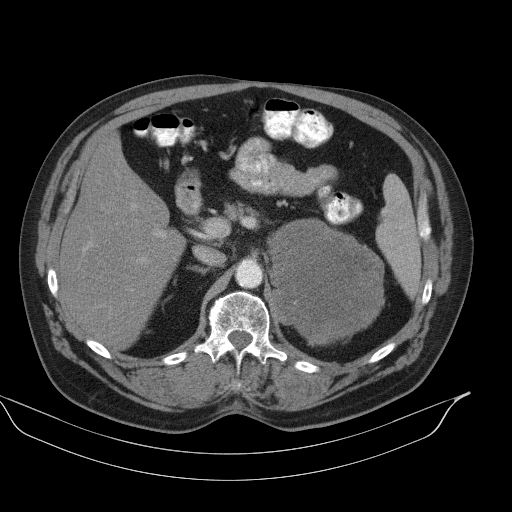
Contrast-enhanced abdominal CT, one axial slice. Slice 66 of 92 in the series (ordered by position). Reconstruction kernel B41s. 130 kVp. Soft-tissue window (W 400 / L 40 HU). 512 × 512 image matrix, field of view 449 × 449 mm. Male patient, age 56 years. Case-level facts recorded for this patient, not image findings: diagnosis: adrenocortical carcinoma; tumour side: left adrenal; tumour size at pathology: 15 cm; Ki-67 index: 35 %; stage (as recorded): 4.
Annotated regions visible in this slice (semi-automatic segmentation, software-assisted and operator-edited):
- mass: bounding box <269,219,383,341> (left, top, right, bottom; pixels)